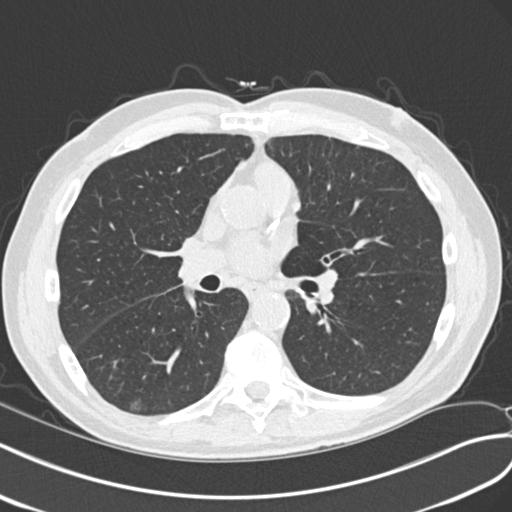
Chest CT (low-dose screening protocol), one axial image. Second annual screen. Lung window (W 1500 / L -600 HU). Standard (soft-tissue) reconstruction kernel (B30f). 120 kVp. Slice 109 of 240 in the series. Male participant, aged 68 years at enrolment.
Expert reader's lesion annotation, bounding box <107,382,157,420> (left, top, right, bottom; pixels). The screening reader recorded 4 non-calcified nodules or masses ≥4 mm on this exam (right upper lobe, left upper lobe, right upper lobe, right lower lobe); which of them this box marks is not recorded. Official screen result: positive, other. Participant outcome: lung cancer diagnosed 653 days after this screen (after the third annual screen) — non-small cell carcinoma, right lower lobe, poorly differentiated (G3), stage IA (AJCC 6th edition), 23 mm at pathology.